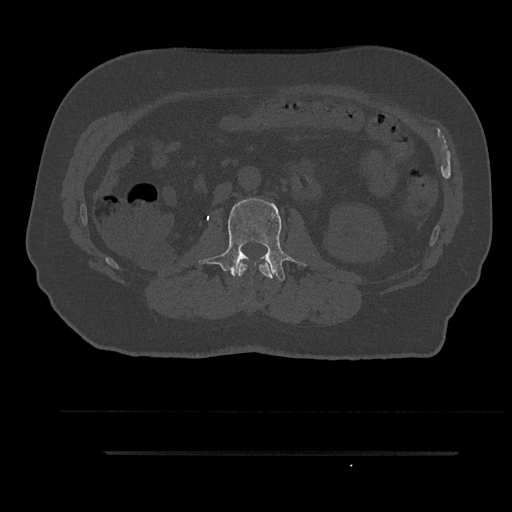
CT including the spine, one axial slice; slice 119 of 797 in the series (ordered by position); bone window (W 1800 / L 400 HU); 0.5 mm slice thickness; 512 × 512 image matrix, field of view 432 × 432 mm. Patient: male, 63 years. Case-level facts recorded for this patient, not image findings: primary cancer: renal.
Structures marked on this image (semi-automatically segmented with operator editing):
- L1 vertebra: bounding box [x1, y1, x2, y2] px = [237, 259, 274, 279]
- L2 vertebra: [199, 198, 306, 281]